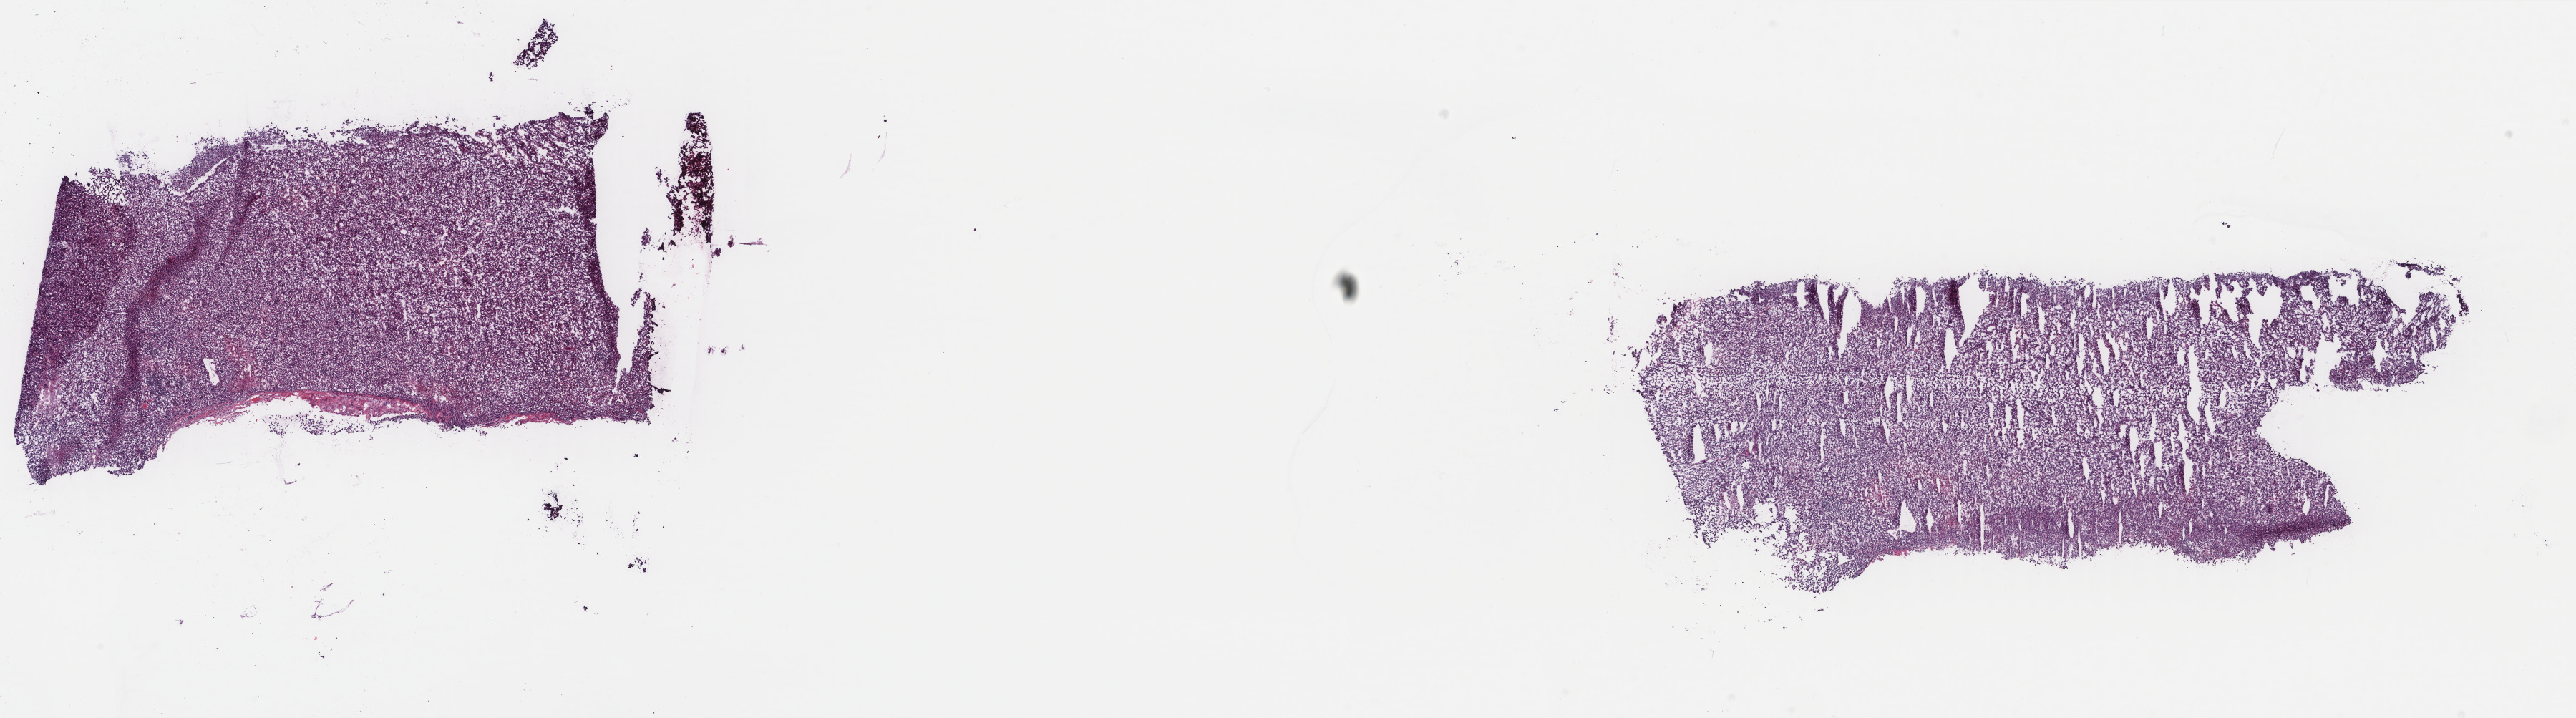
Digitized H&E tissue section (whole slide), whole scanned area (about 28.6 x 8.0 mm, slide scanned at 40x) shown as a low-resolution overview. Frozen section. Metastatic tumour sample, sampled site not recorded. Female, age 72 years at initial diagnosis. Slide review estimates, as recorded: tumour cells 85%, tumour nuclei 85%, normal cells 0%, stromal cells 12%, necrosis 3%. Infiltration values recorded for this section: lymphocyte infiltration 3%, monocyte infiltration 1%, neutrophil infiltration 1%.
This section: metastatic tumour tissue. Patient diagnosis: Malignant melanoma, NOS.